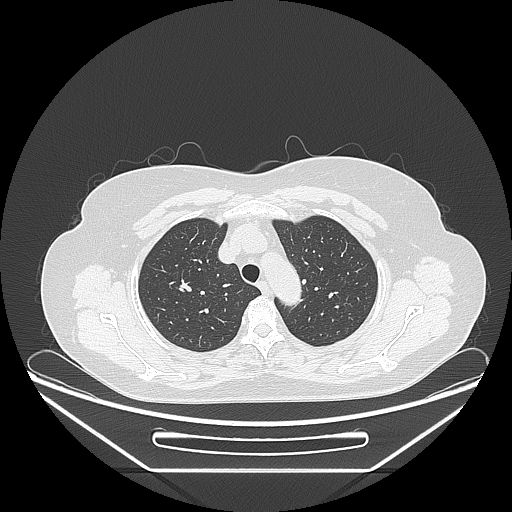
Chest CT, one axial slice; slice 194 of 236 in the series (ordered by position); lung window (W 1500 / L -600 HU); 1.25 mm slice thickness; 512 × 512 image matrix, field of view 433 × 433 mm. Female patient, age 60 years. From the clinical record (not read from this slice): clinical TNM (as recorded): T1c N0 M0; histopathological grade: G2-3.
Annotated regions visible in this slice (bounding box drawn by a radiologist):
- lung tumour (recorded histology: adenocarcinoma): box from (x=173, y=271) to (x=193, y=305) px